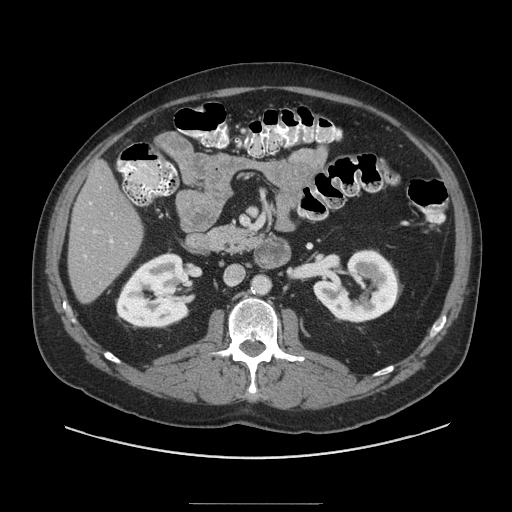
Contrast-enhanced abdominal CT (liver protocol), one axial slice; reconstruction kernel STANDARD; soft-tissue window (W 400 / L 40 HU); 2.5 mm slice thickness; 512 × 512 image matrix. From the clinical record (not read from this slice): diagnosis: hepatocellular carcinoma (patient treated with transarterial chemoembolisation; whether this scan precedes or follows treatment is not stated here); TNM stage (as recorded): Stage-I; Child-Pugh class: A; tumour differentiation: well differentiated; tumour nodularity: uninodular.
Outlined on this slice (semi-automatic segmentation, software-assisted and operator-edited):
- liver parenchyma outside the tumour (the mass and vessels are separate outlines, so this box may not span the whole liver): bounding box <68,162,142,302> (left, top, right, bottom; pixels)
- liver vessels: <84,202,113,258>